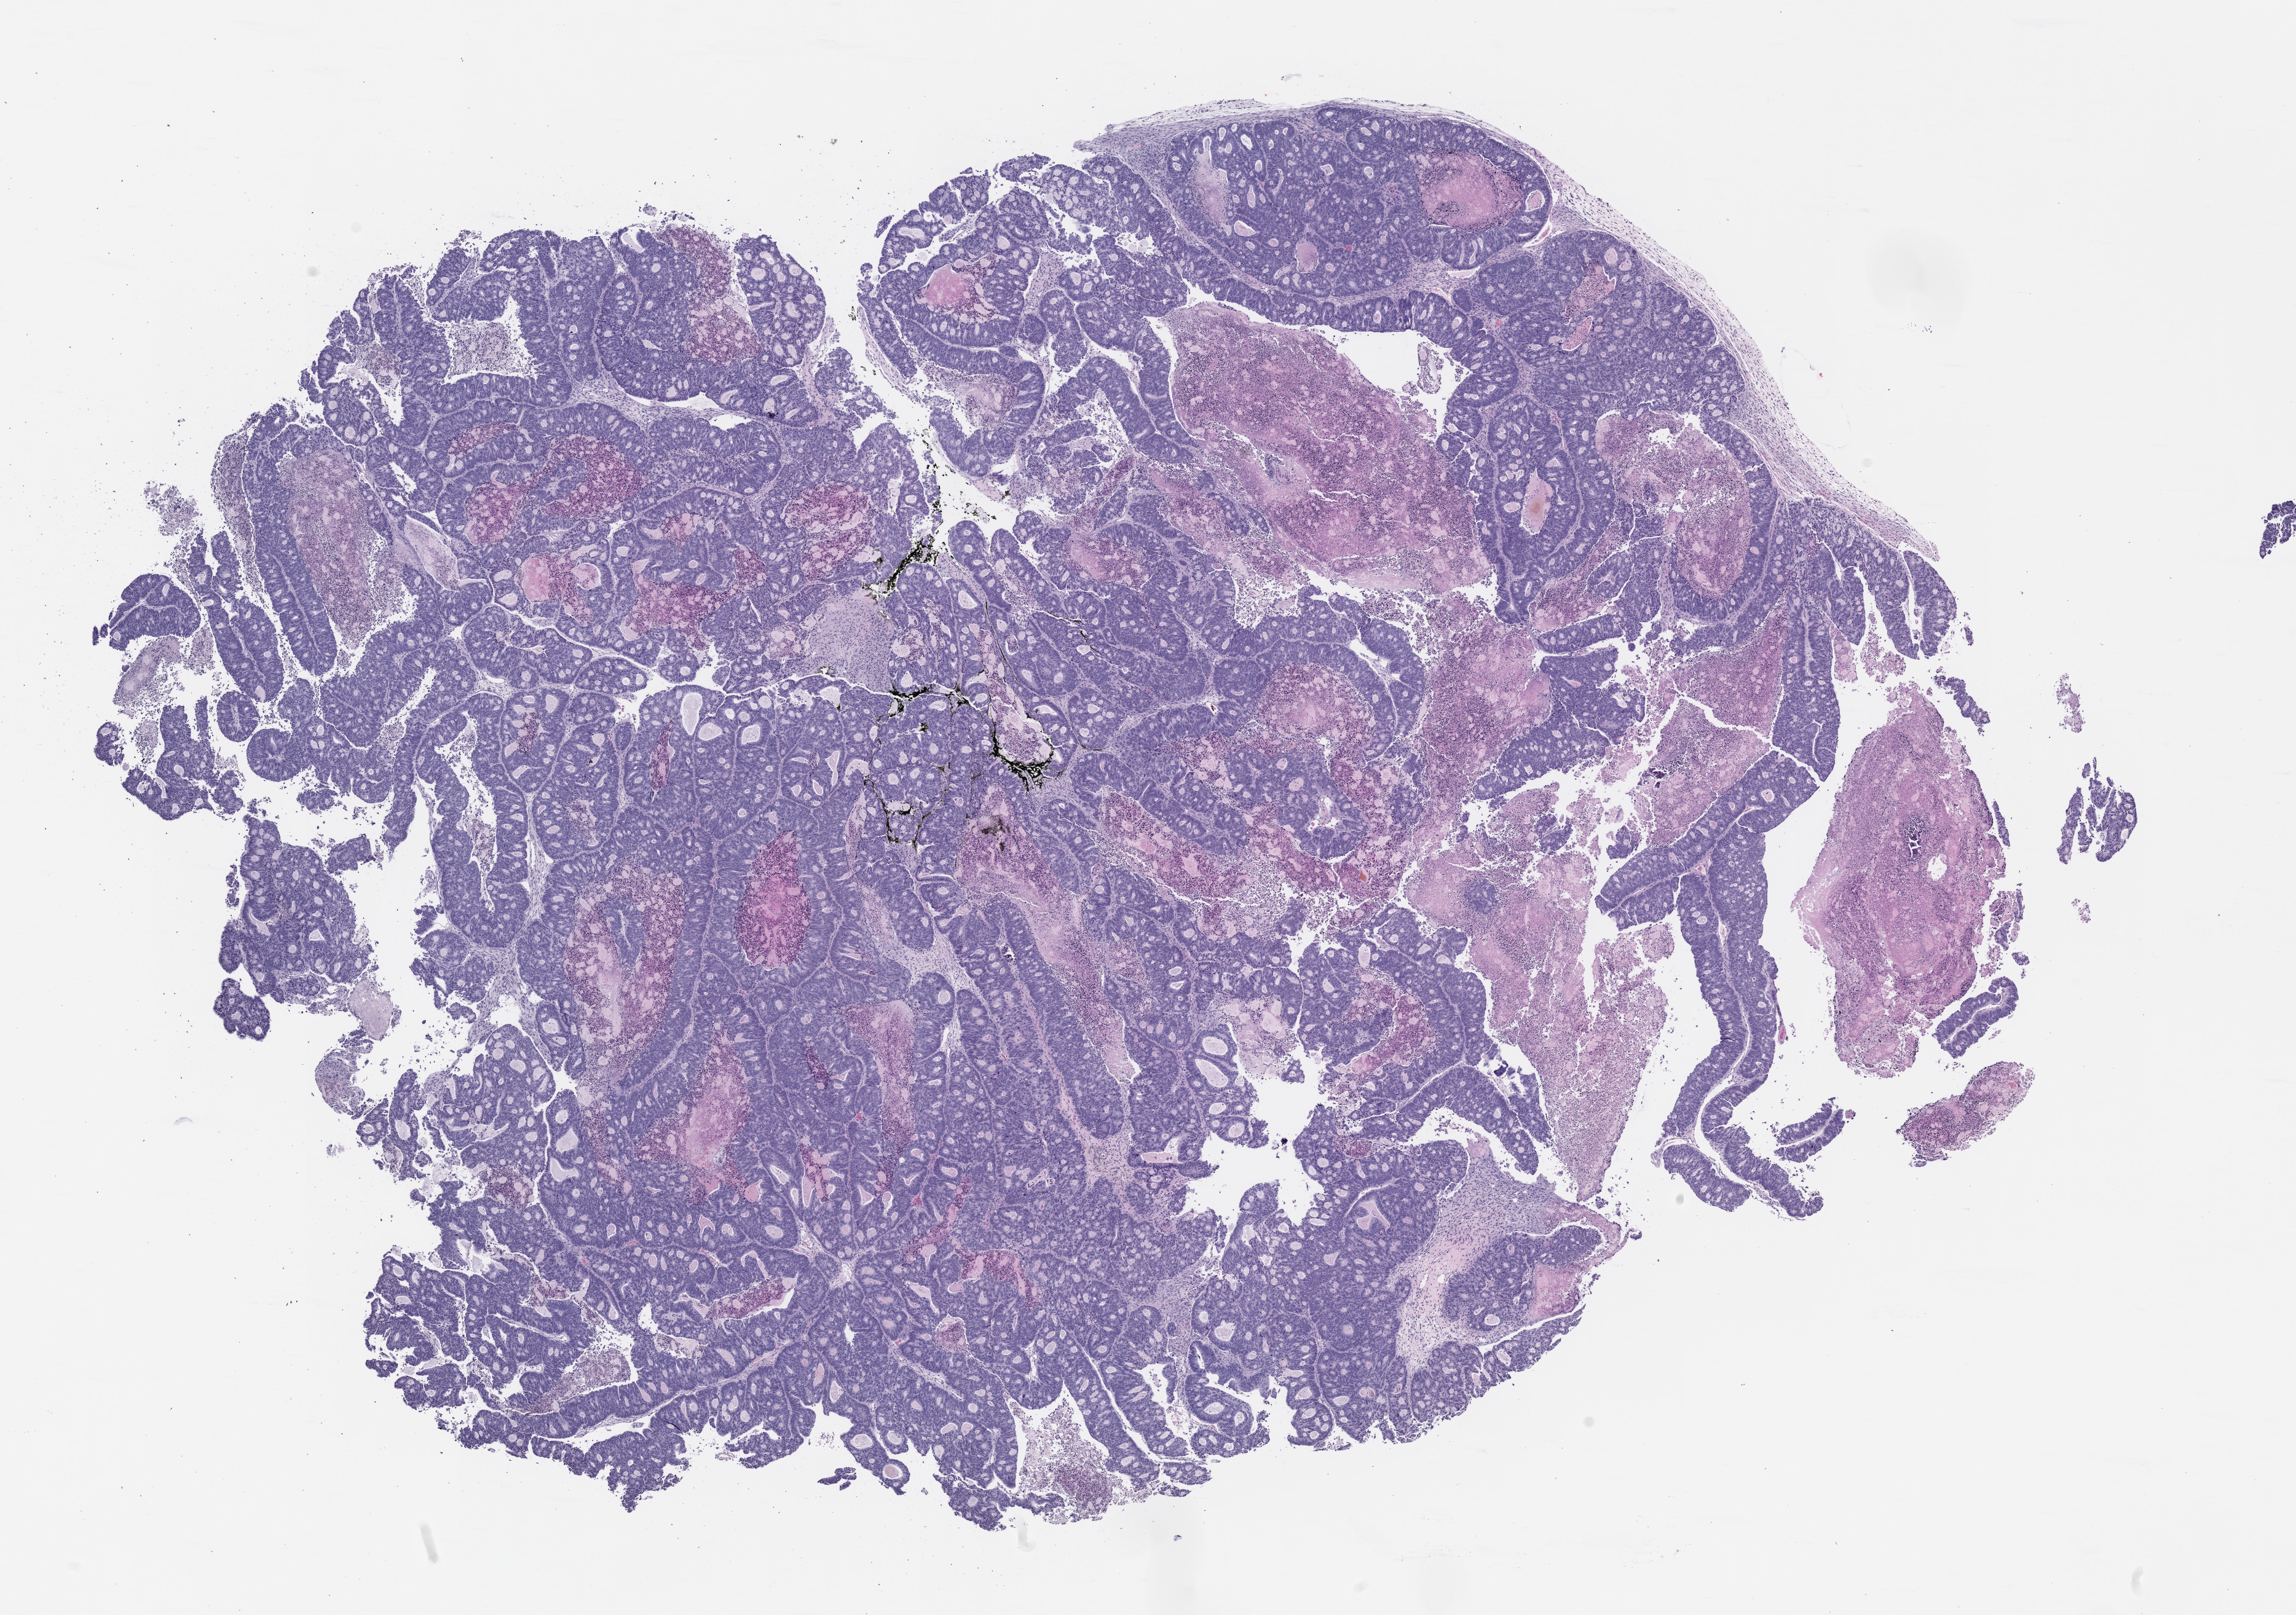
Haematoxylin and eosin whole-slide image of a patient-derived xenograft (PDX) tumor grown in a mouse, passage 2, shown as a low-resolution overview of the whole scanned area (about 15.0 x 10.6 mm), formalin-fixed, paraffin-embedded (FFPE) tissue, tumor site category: colon.
Originating patient diagnosis: Colon Adenocarcinoma.